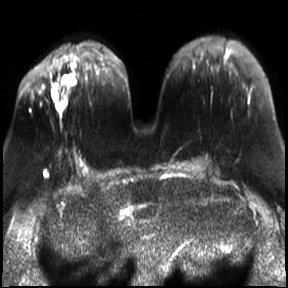
Breast MRI, one axial slice; slice 10 of 30 in the series (ordered by position); diffusion-weighted series; image 2 of 4 stored at this slice position (different b-values; order by instance number); 3 T; 4 mm slice thickness; 288 × 288 image matrix, field of view 340 × 340 mm. Female patient.
Annotated regions visible in this slice (outlined manually by an expert reader):
- tumour on diffusion-weighted imaging: bounding box <51,78,75,98> (left, top, right, bottom; pixels)